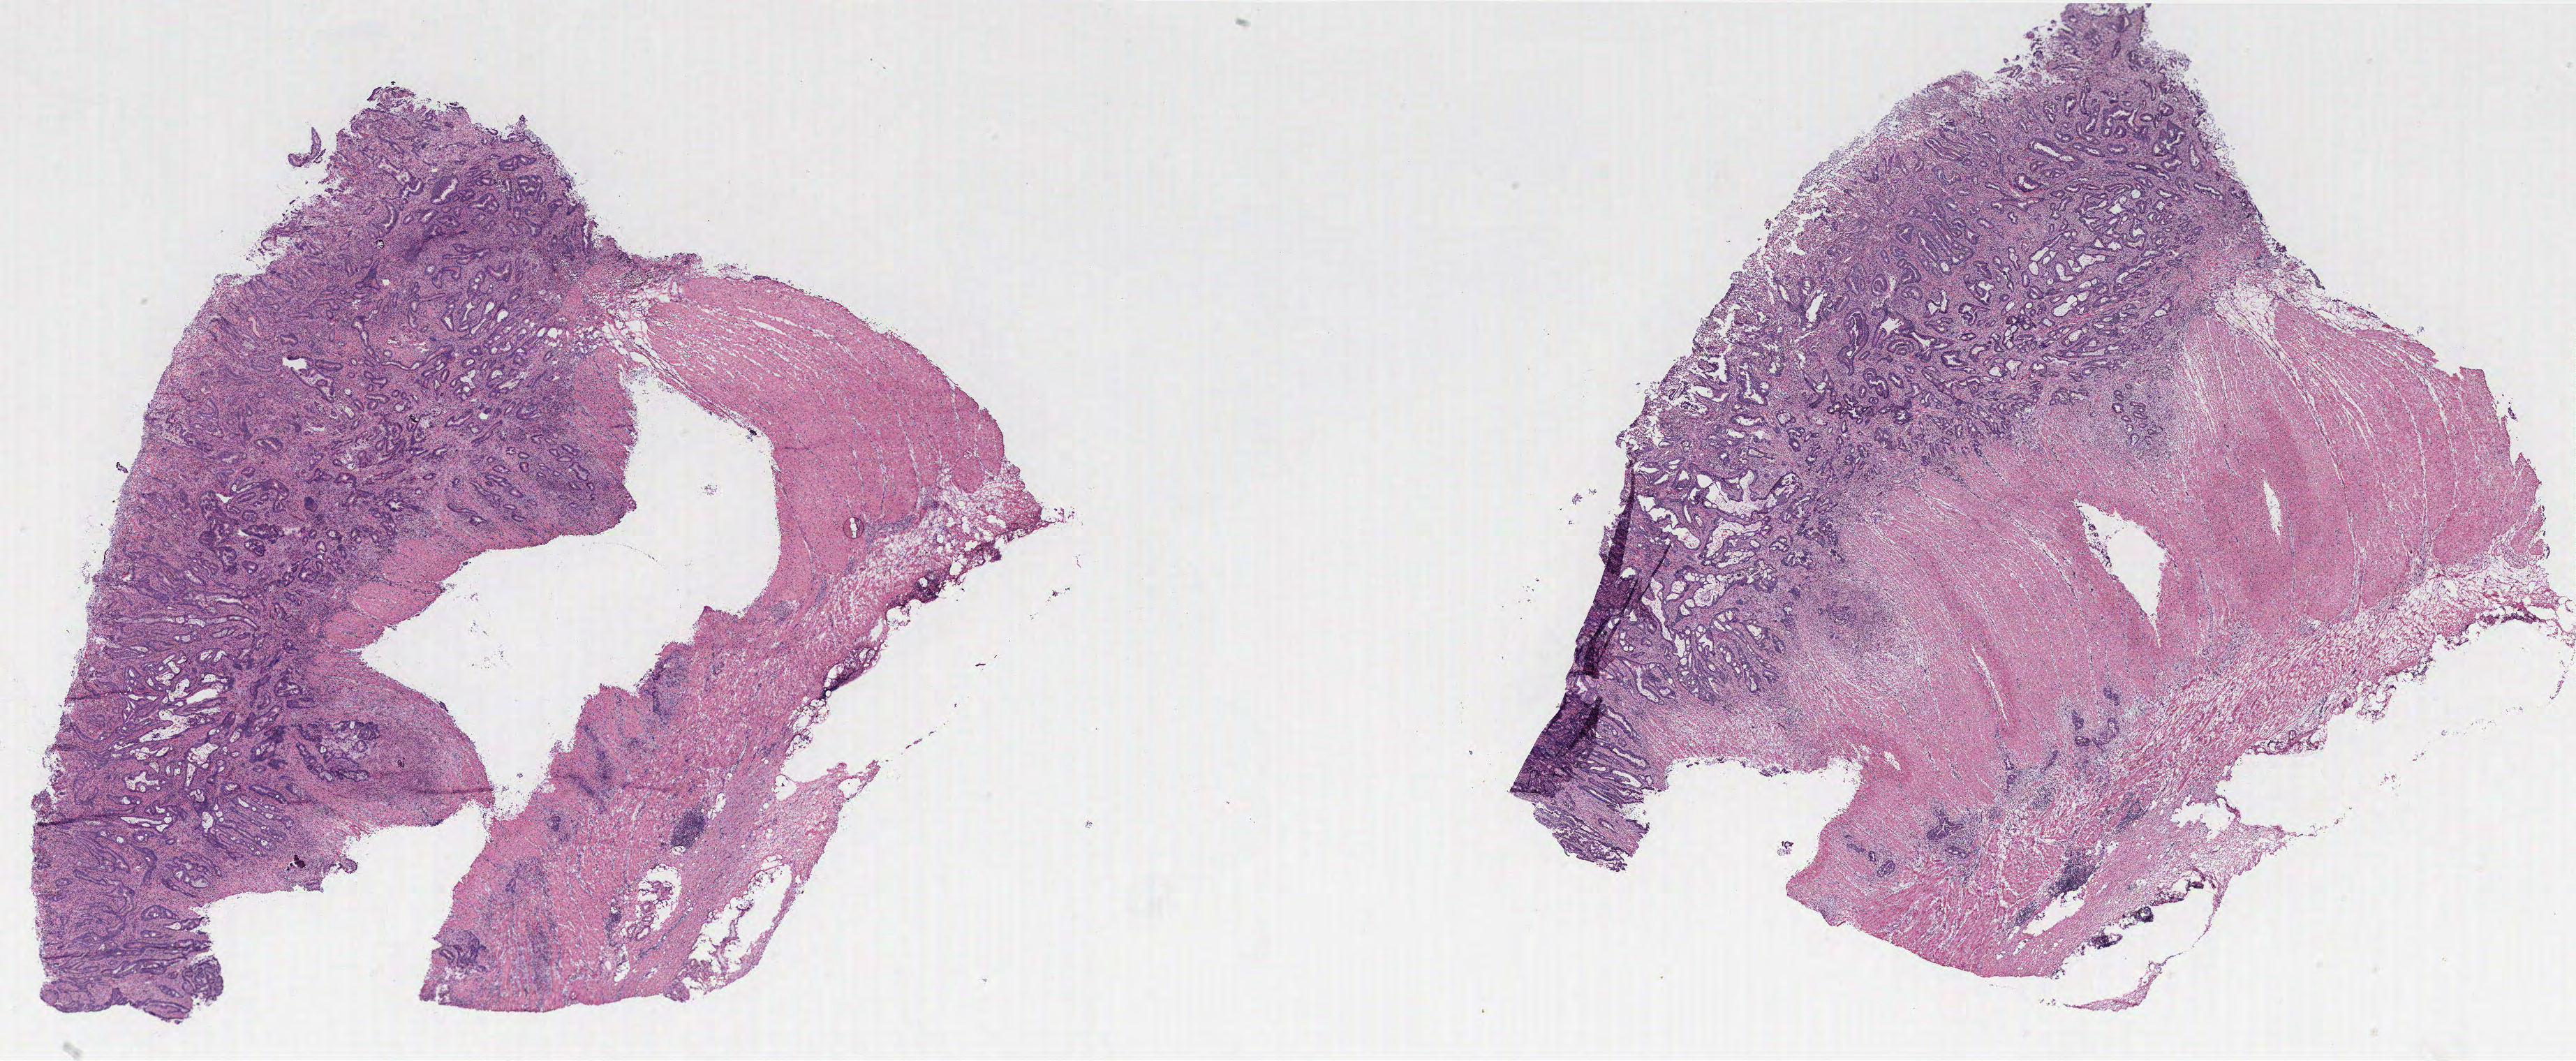
Digitized H&E-stained tissue section (whole slide), a low-resolution overview of the entire scanned area, about 29.5 x 12.2 mm (from a 40x scan). Tumour tissue sample, colon. Patient: female, age 63 years.
Primary tumour site (as recorded): colon. AJCC pathologic stage: IIA. Histologic diagnosis: Adenocarcinoma, NOS.